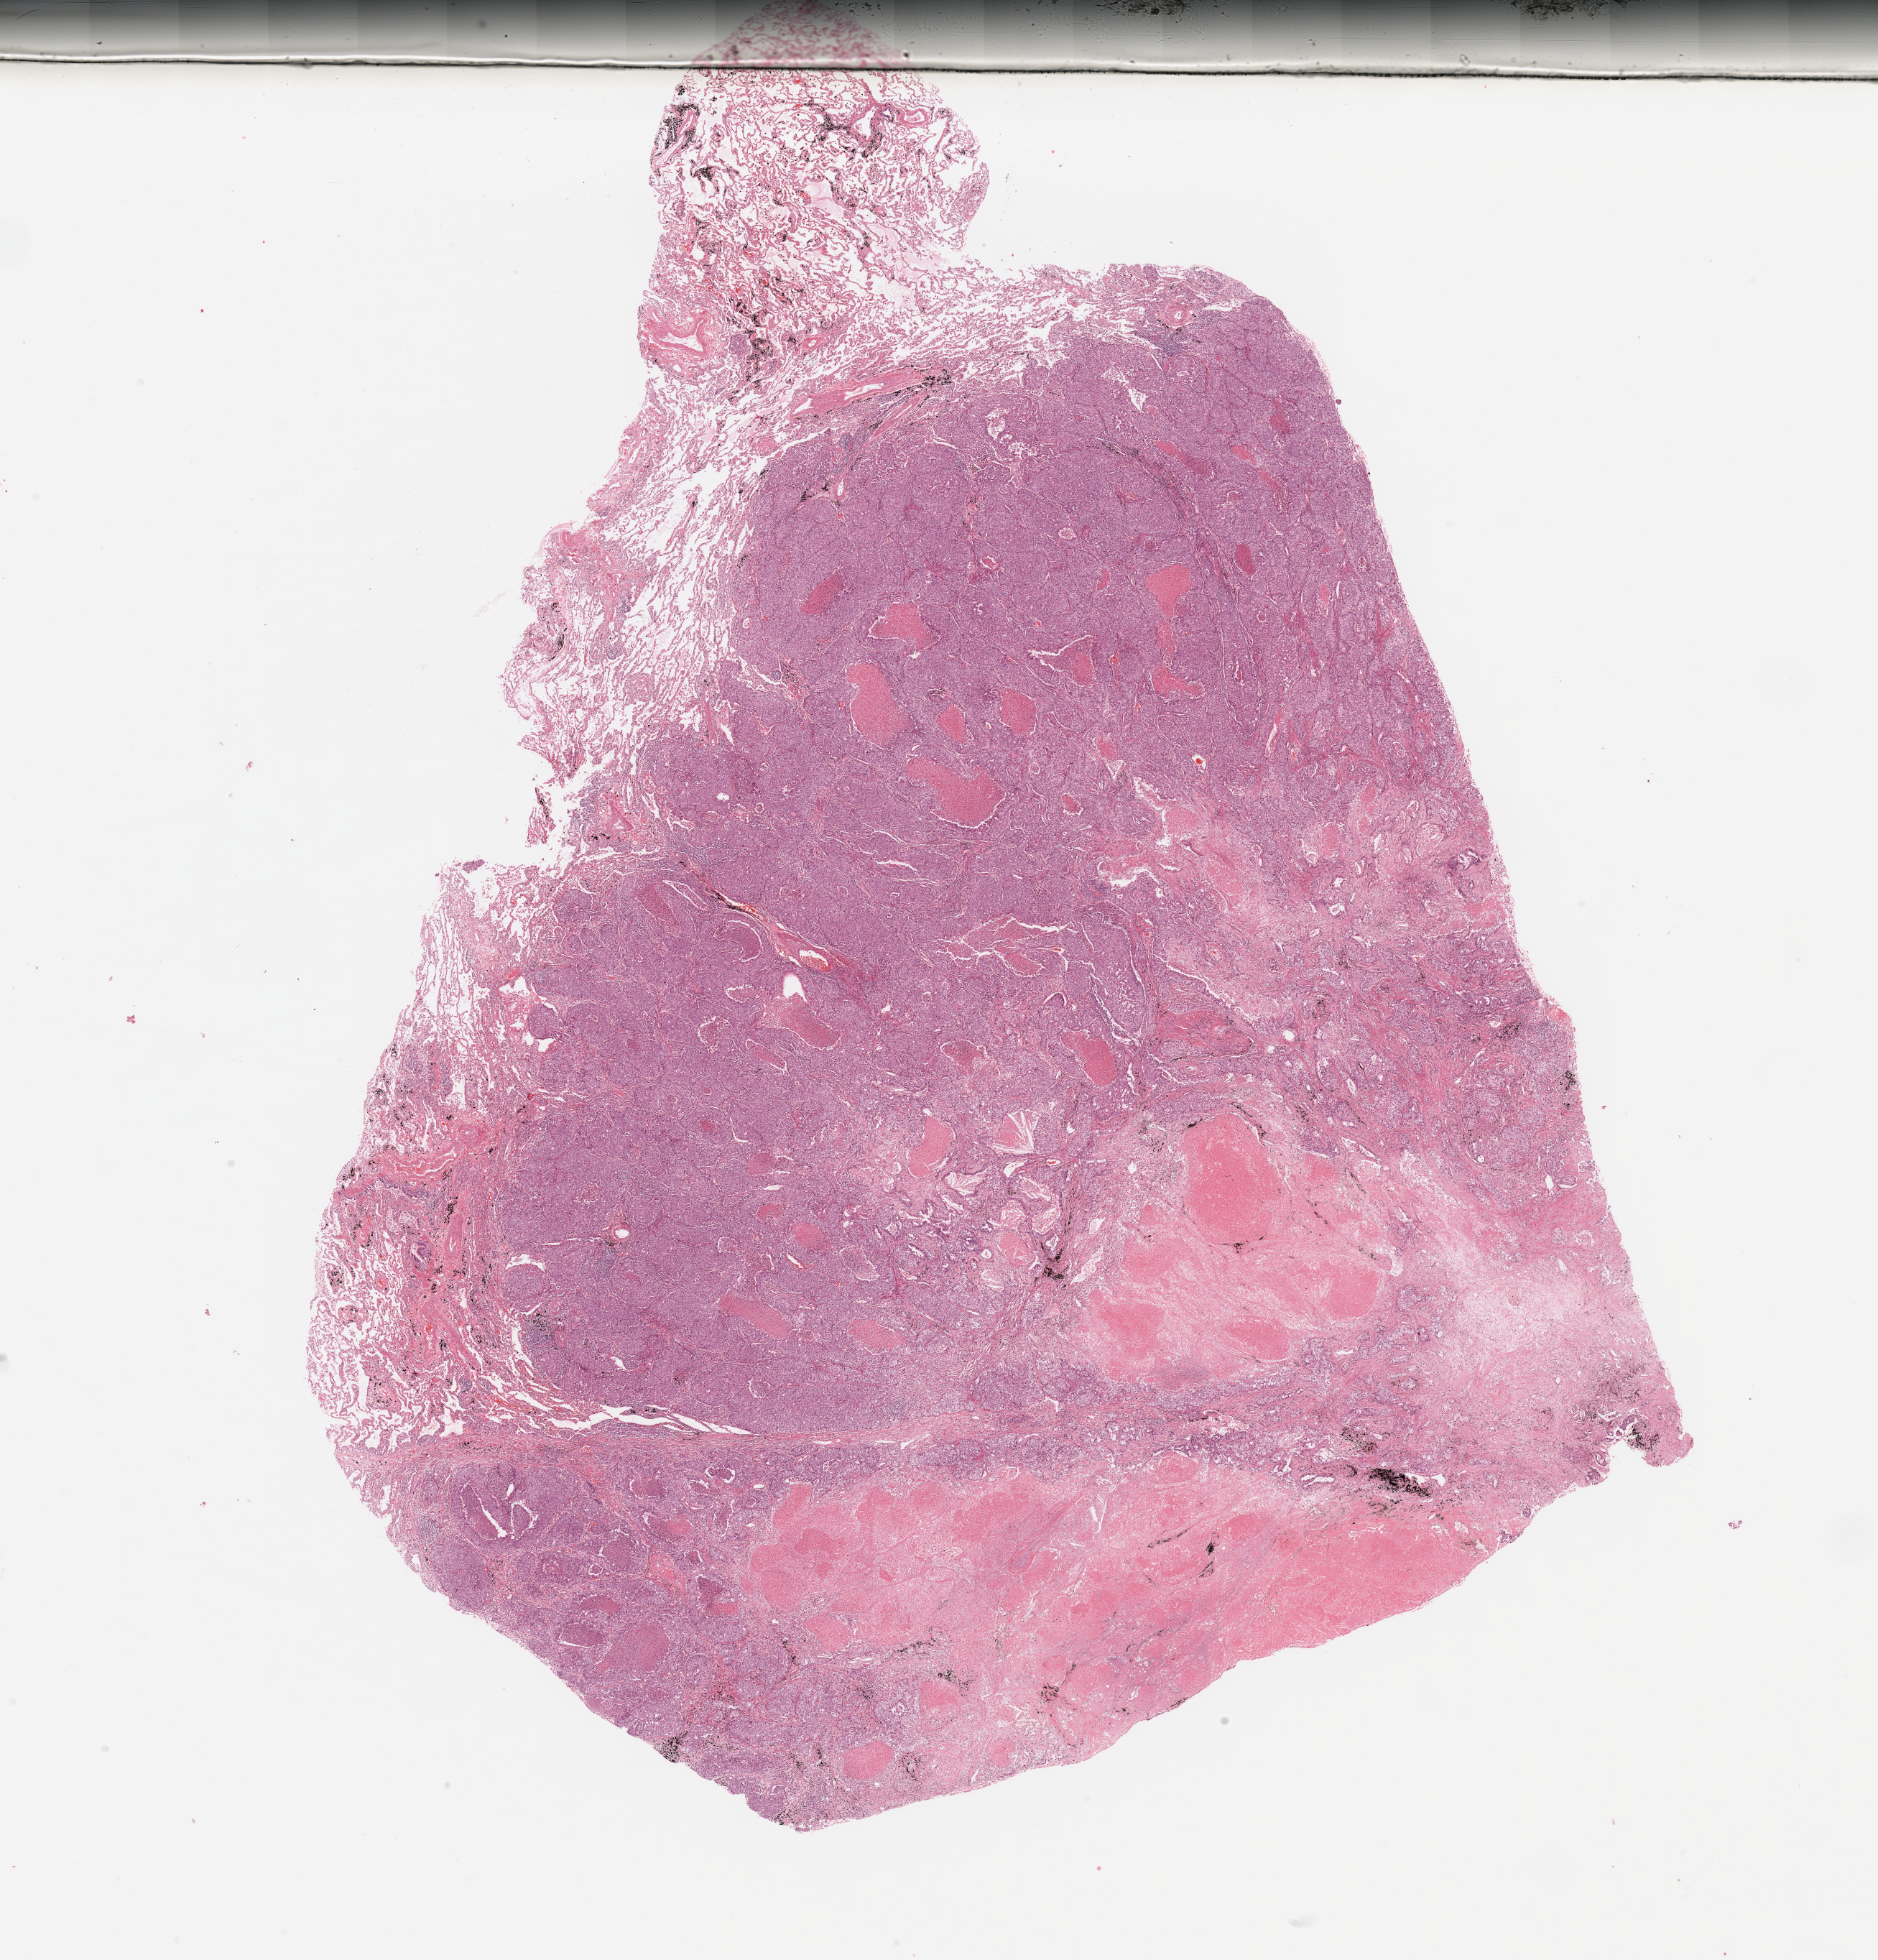
Whole-slide histology image, H&E, whole scanned area (about 20.7 x 21.6 mm, acquisition: 20x scan) shown as a low-resolution overview; lung, tumour tissue. Patient: male, age 55 years.
Histologic diagnosis: Adenocarcinoma, NOS.